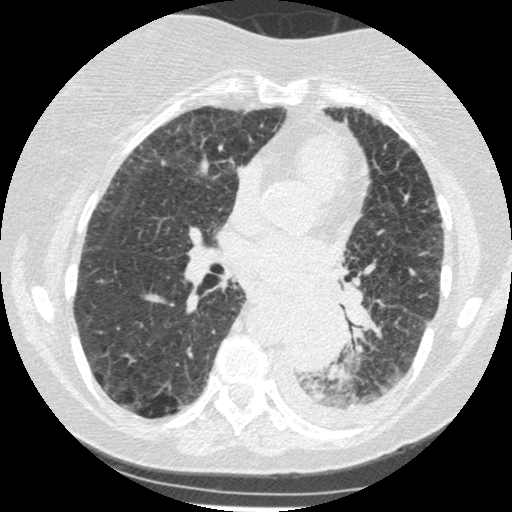
Chest CT (low-dose screening protocol), one axial image; third annual screen; lung window (W 1500 / L -600 HU); 1.25 mm slice thickness; standard (soft-tissue) reconstruction kernel (STANDARD); slice 220 of 341 in the series; 512 × 512 image matrix. Female participant, aged 60 years at enrolment. Former smoker at enrolment.
Expert reader's lesion annotation, box from (x=273, y=305) to (x=342, y=375) px. The exam's reader record, not a measurement of the box and not confirmed to be the same lesion: non-calcified nodule or mass ≥4 mm, left lower lobe, 54 × 38 mm, smooth margins, soft tissue attenuation, pre-existing on the prior screen: yes; interval growth: yes. Official screen result: positive, other. Lung cancer was diagnosed 15 days after this screen: small cell carcinoma, NOS, left lower lobe, undifferentiated (G4), stage IV (AJCC 6th edition), 69 mm at pathology.